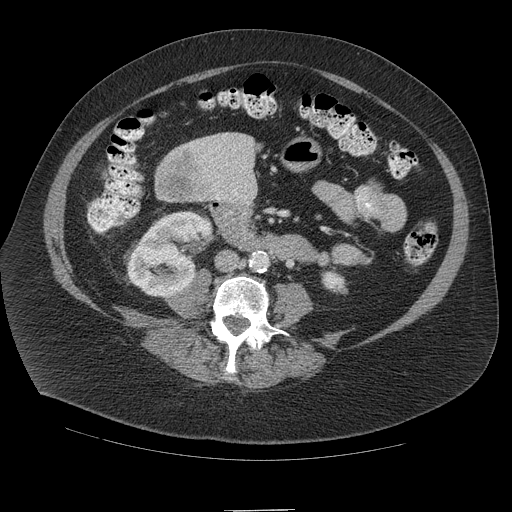
Contrast-enhanced abdominal CT (liver protocol), one axial slice. Slice 24 of 109 in the series (ordered by position). Reconstruction kernel STANDARD. Soft-tissue window (W 400 / L 40 HU). 2.5 mm slice thickness. 512 × 512 image matrix, field of view 420 × 420 mm. From the clinical record (not read from this slice): diagnosis: hepatocellular carcinoma (patient treated with transarterial chemoembolisation; whether this scan precedes or follows treatment is not stated here); TNM stage (as recorded): Stage-IVB; Child-Pugh class: A; tumour differentiation: poorly differentiated; tumour nodularity: multinodular.
Structures marked on this image (semi-automatic segmentation, software-assisted and operator-edited):
- liver parenchyma outside the tumour (the mass and vessels are separate outlines, so this box may not span the whole liver): bounding box <195,132,254,161> (left, top, right, bottom; pixels)
- liver vessels: <202,144,220,147>